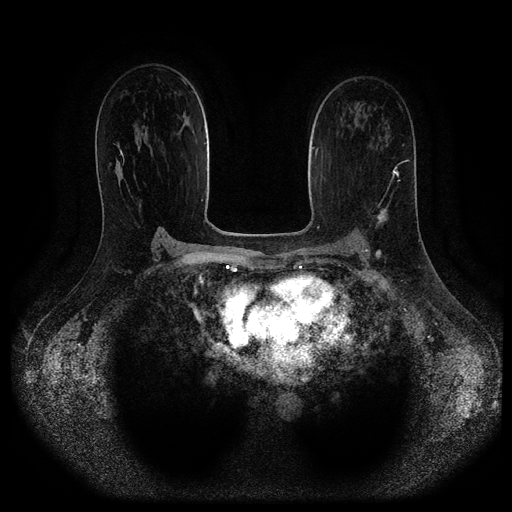
Breast MRI (dynamic contrast-enhanced, multi-phase), one axial slice; position 64 of 116 along the scan axis; dynamic contrast-enhanced series, time point 2 of 5 at this slice position (early post-contrast); 1.5 T; TE 2.6 ms, TR 5.3 ms; 2 mm slice thickness; 512 × 512 image matrix, field of view 370 × 370 mm. Patient: female, 45 years.
Annotated regions visible in this slice (semi-automatically segmented with operator editing):
- breast lesion (labelled 'tumour' in the annotation; benign lesions carry a separate 'benign' label): bounding box <376,206,389,225> (left, top, right, bottom; pixels)